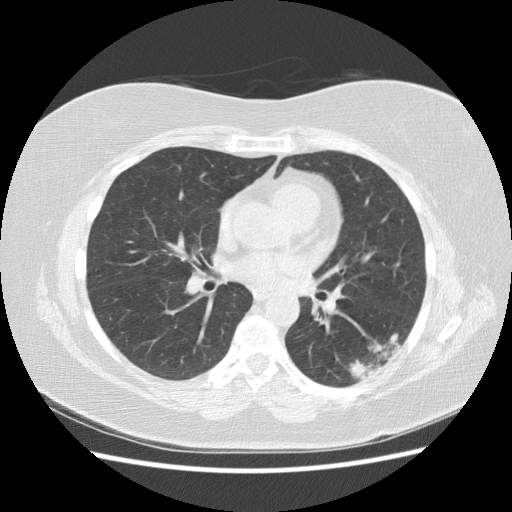
Chest CT (low-dose screening protocol), one axial image. Third screening round (two years after baseline). Lung window (W 1500 / L -600 HU). 2.5 mm slice thickness. Standard (soft-tissue) reconstruction kernel (STANDARD). 120 kVp. Slice 80 of 151 in the series. 512 × 512 image matrix. Female, age 57 years at enrolment. Current smoker at enrolment.
Lesion marked by an expert reader, box from (x=334, y=325) to (x=409, y=388) px. The exam's reader record, not a measurement of the box and not confirmed to be the same lesion: non-calcified nodule or mass ≥4 mm, left lower lobe, 40 × 20 mm, poorly defined margins, mixed attenuation, pre-existing on the prior screen: yes; interval growth: yes. Lung cancer was diagnosed 55 days after this screen: squamous cell carcinoma, NOS, left lower lobe, poorly differentiated (G3), stage IB (AJCC 6th edition), 40 mm at pathology.